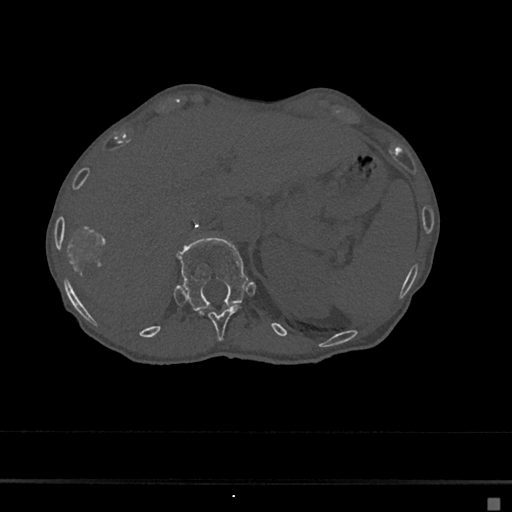
CT including the spine, one axial slice; slice 139 of 797 in the series (ordered by position); 120 kVp; bone window (W 1800 / L 400 HU); 0.5 mm slice thickness; 512 × 512 image matrix. Female patient, age 68 years. From the clinical record (not read from this slice): primary cancer: renal.
Structures marked on this image (semi-automatic segmentation, software-assisted and operator-edited):
- T11 vertebra: bounding box (x1, y1, x2, y2) in pixels: (199, 306, 241, 340)
- T12 vertebra: (177, 237, 249, 311)